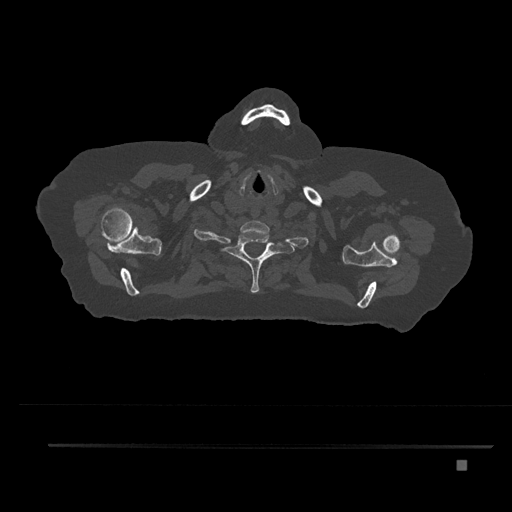
CT including the spine, one axial slice. Position 702 of 797 along the scan axis. Bone window (W 1800 / L 400 HU). 0.5 mm slice thickness. 512 × 512 image matrix. Female patient, age 76 years. Case-level facts recorded for this patient, not image findings: primary cancer: lung.
Structures marked on this image (semi-automatically segmented with operator editing):
- T1 vertebra: bounding box [x1, y1, x2, y2] px = [223, 232, 283, 293]